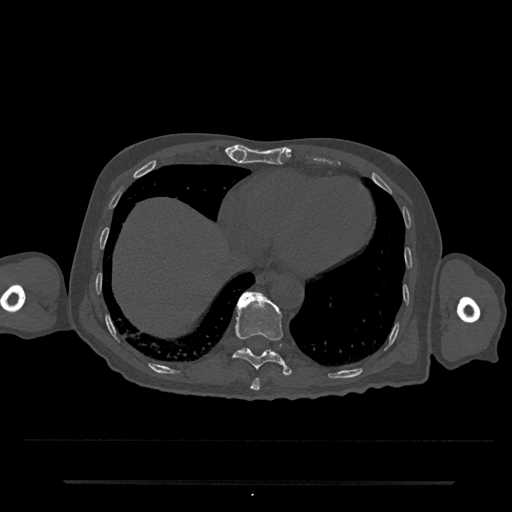
CT including the spine, one axial slice; slice 308 of 797 in the series (ordered by position); reconstruction kernel Br40s/3; bone window (W 1800 / L 400 HU); 0.5 mm slice thickness; 512 × 512 image matrix, field of view 427 × 427 mm. Male patient, age 74 years. Case-level facts recorded for this patient, not image findings: primary cancer: prostate.
Annotated regions visible in this slice (semi-automatic segmentation, software-assisted and operator-edited):
- T10 vertebra: box from (x=233, y=292) to (x=292, y=376) px
- T11 vertebra: (x=242, y=292)–(x=262, y=350)
- T9 vertebra: (x=250, y=378)–(x=260, y=391)